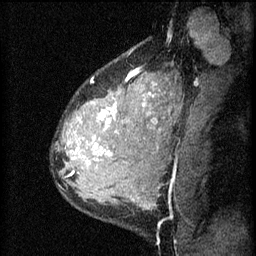
Breast MRI (dynamic contrast-enhanced), one sagittal slice; position 45 of 60 along the scan axis; 3 images stored at this slice position (order not interpretable as contrast timing); 1.5 T; TE 4.2 ms, TR 8.2 ms; 256 × 256 image matrix. Female patient, age 37 years.
Outlined on this slice (semi-automatically segmented with operator editing):
- analysis volume of interest (the breast-tissue region the enhancement analysis was run in; not a lesion): box from (x=56, y=78) to (x=140, y=181) px
- tumour enhancement mask (voxels above the 70 % enhancement threshold inside the analysis volume of interest): (x=71, y=78)–(x=130, y=175)